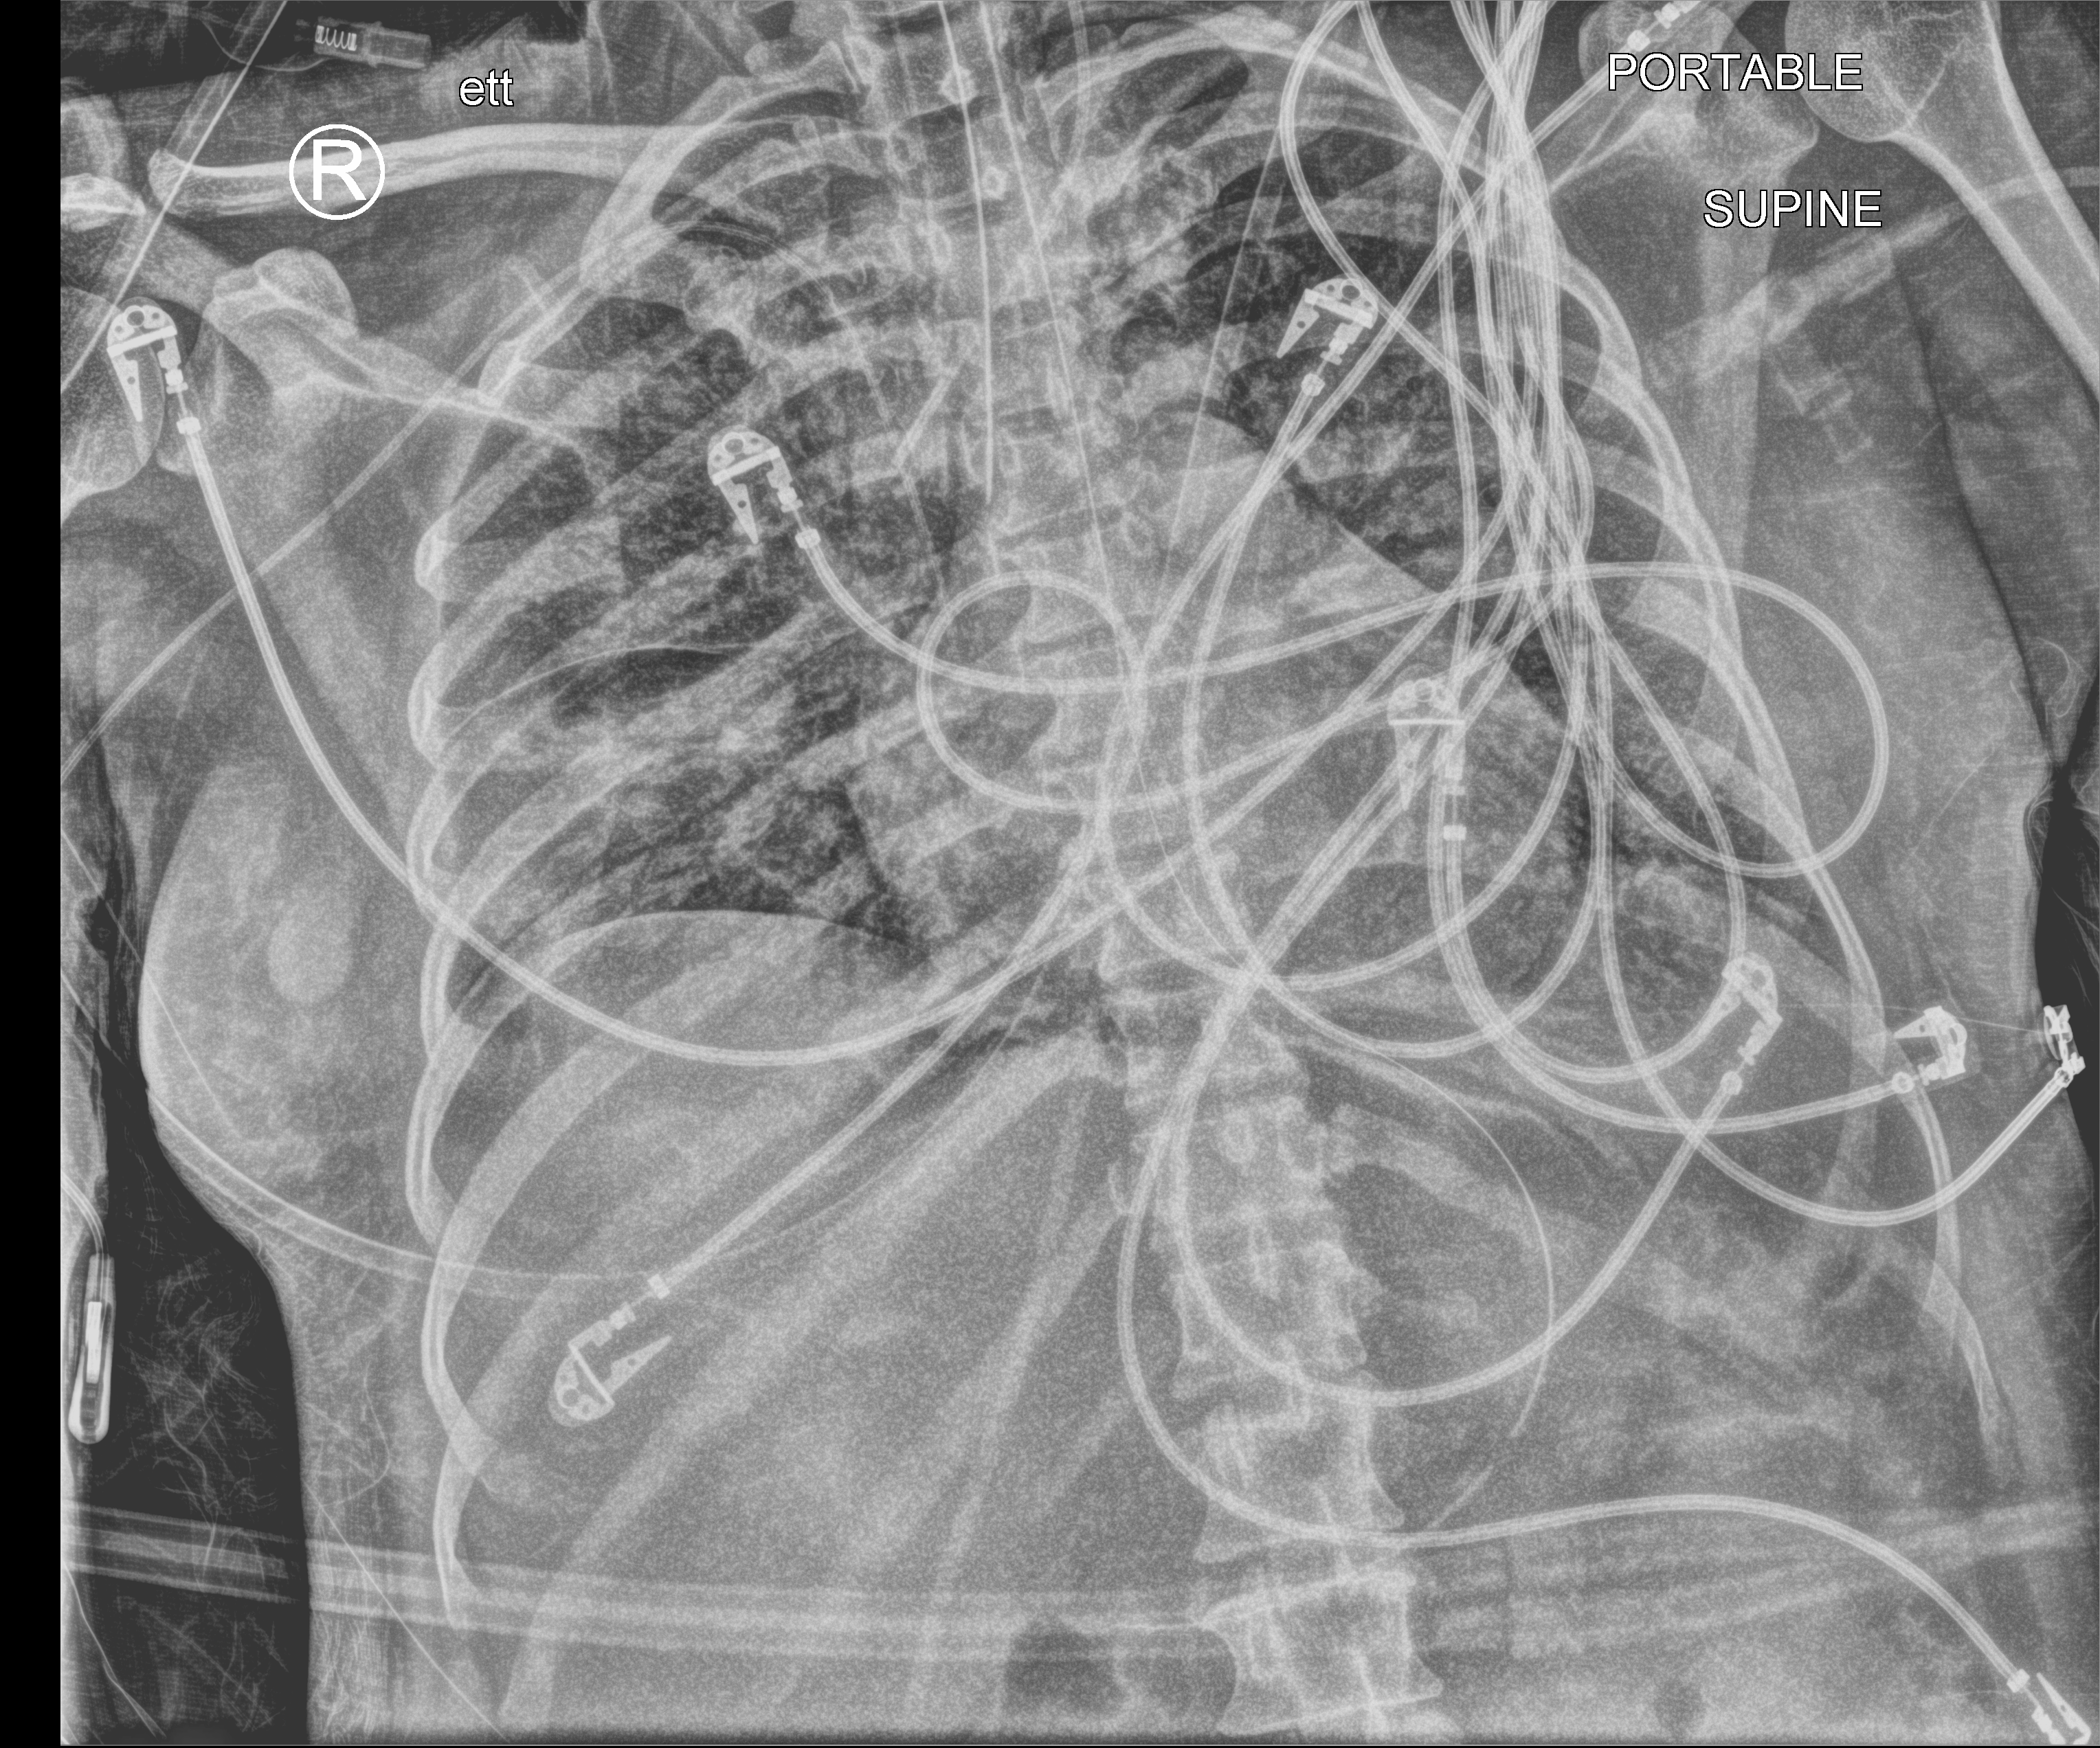
Portable chest radiograph, anteroposterior (AP) projection. Patient hospitalised with COVID-19; female, aged 18–59 years.
From the hospital-stay record, not from the radiograph (when in the stay this image was taken is not recorded): mechanically ventilated during this hospital stay: yes; admitted to intensive care during this hospital stay: yes.